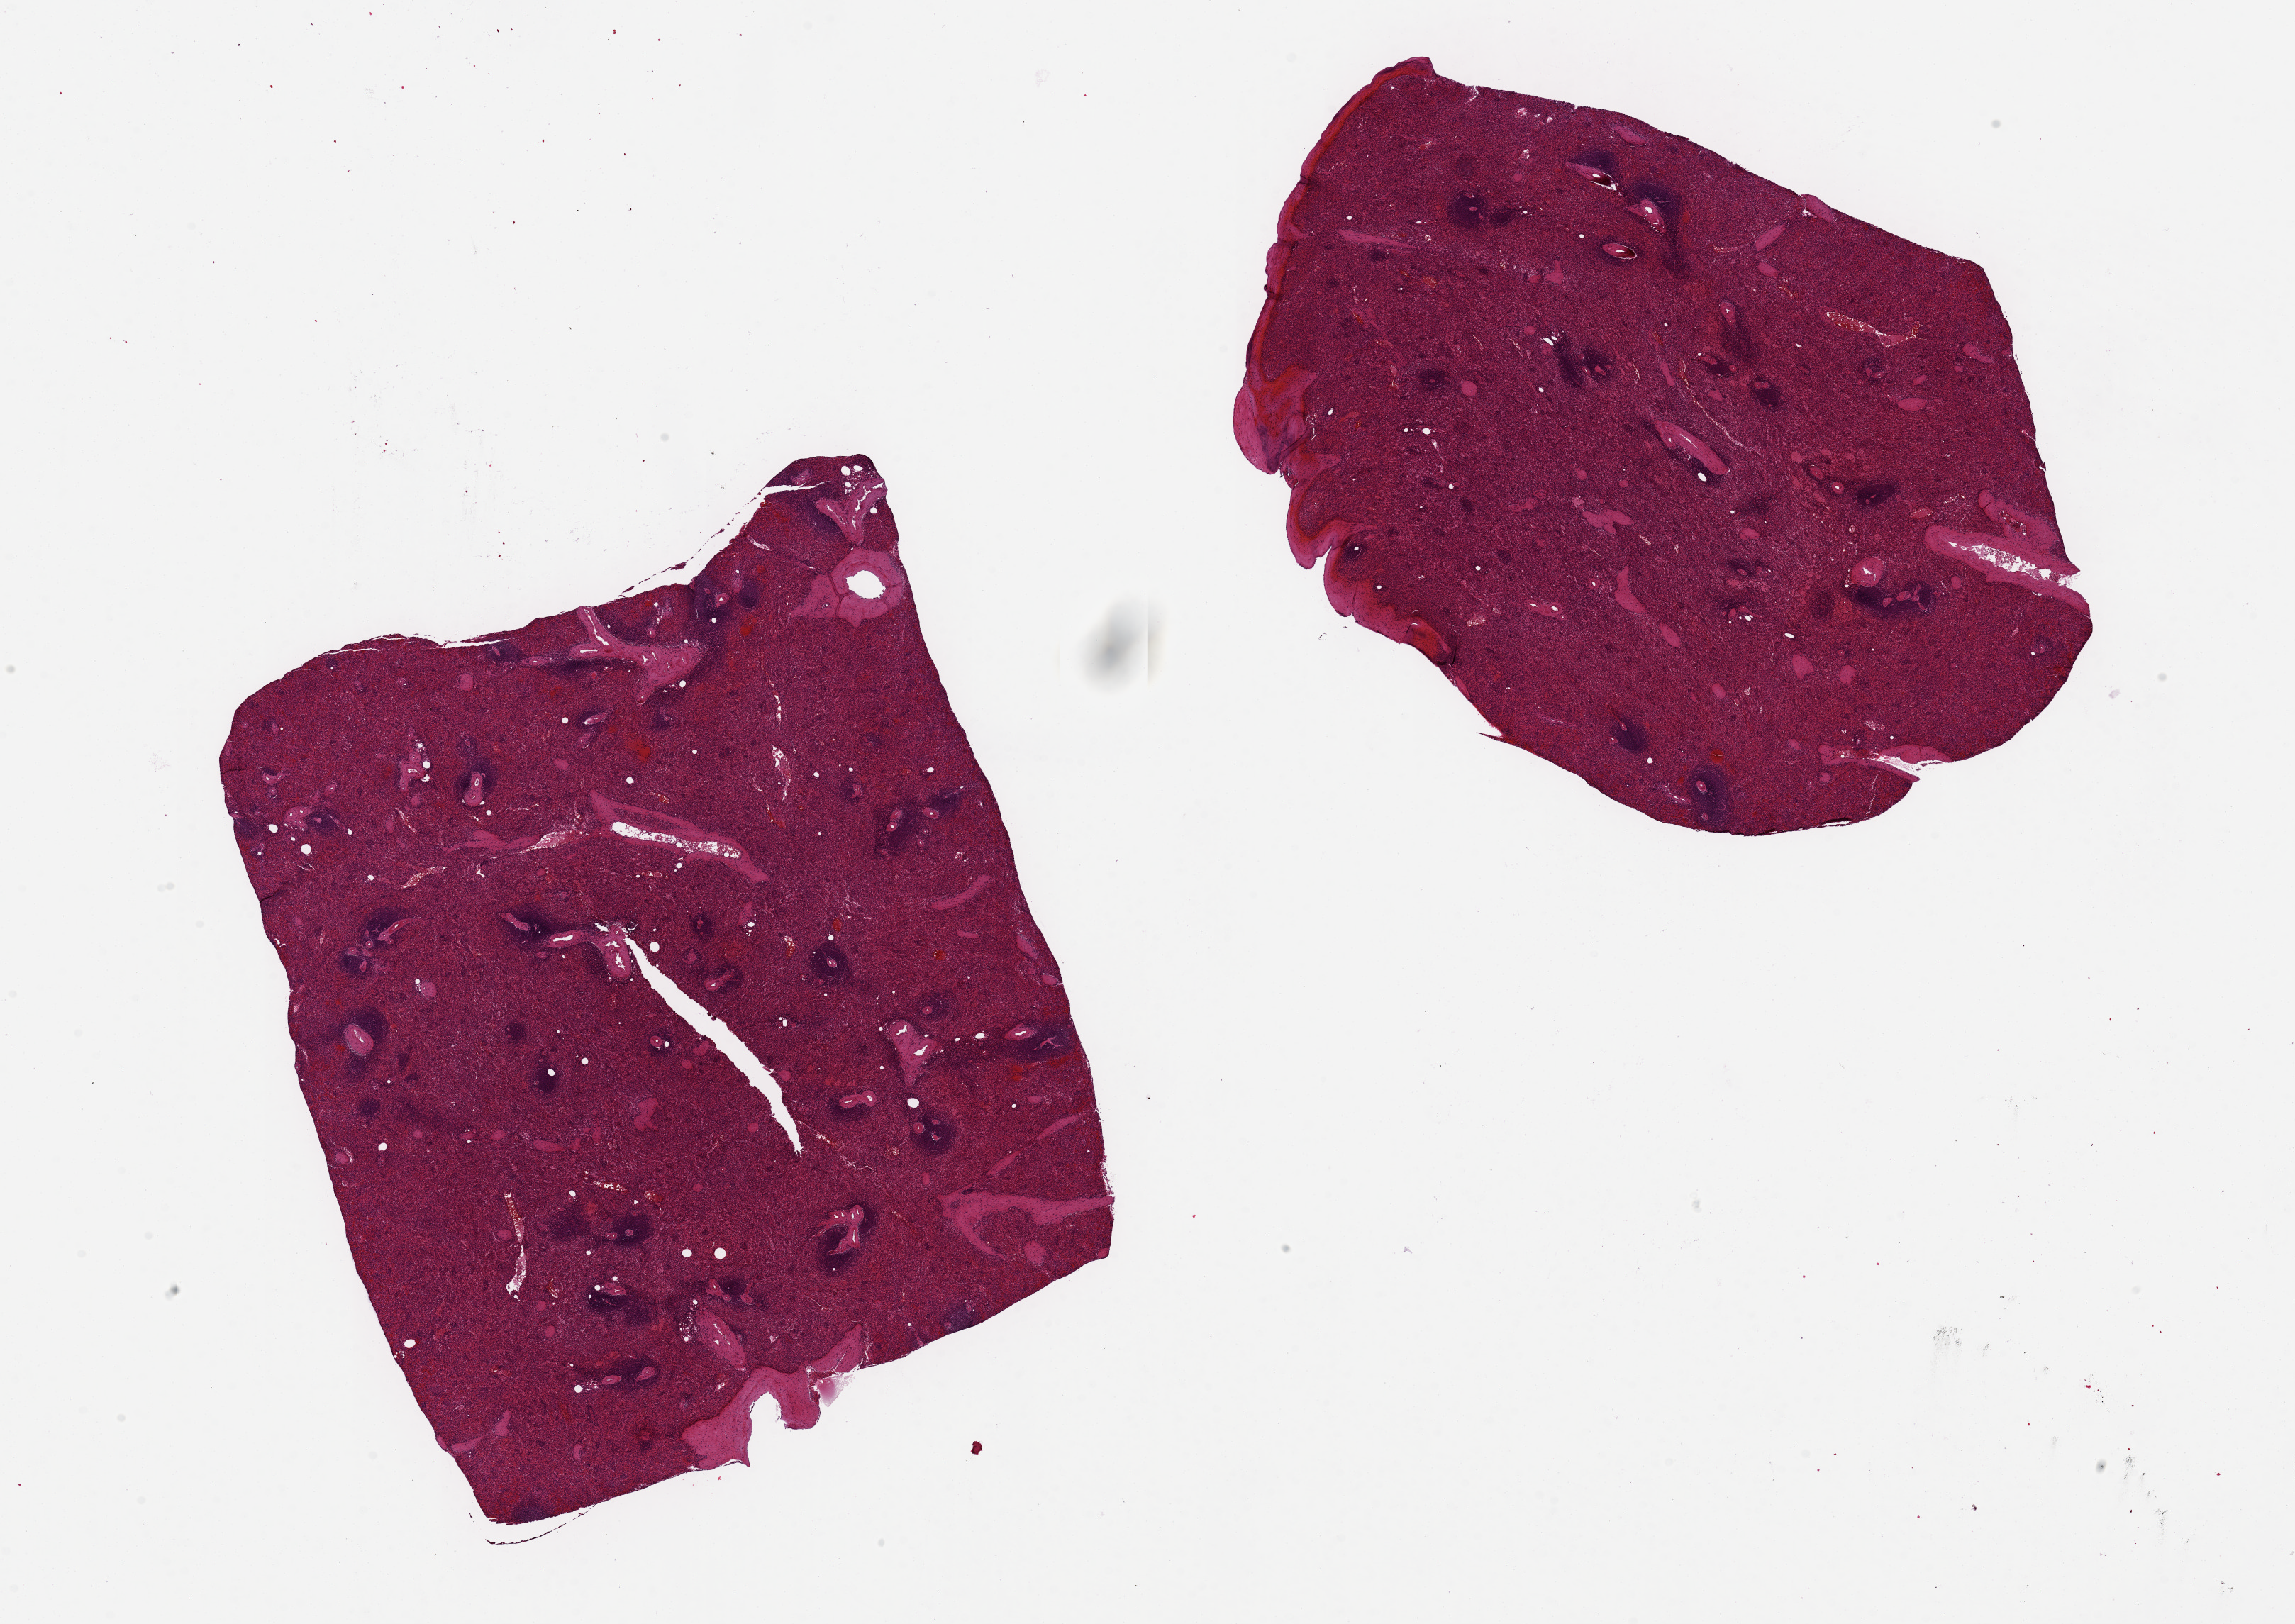
Whole-slide image, H&E stain, brightfield, a low-resolution overview of the entire scanned area, about 25.6 x 18.1 mm (acquisition: 20x scan). PAXgene-fixed, paraffin-embedded tissue. Sampled site (target tissue): spleen. Tissue donor sample. Male donor.
• review note (as recorded): 2 pieces 9x8 & 9x7 mm; mild congestion